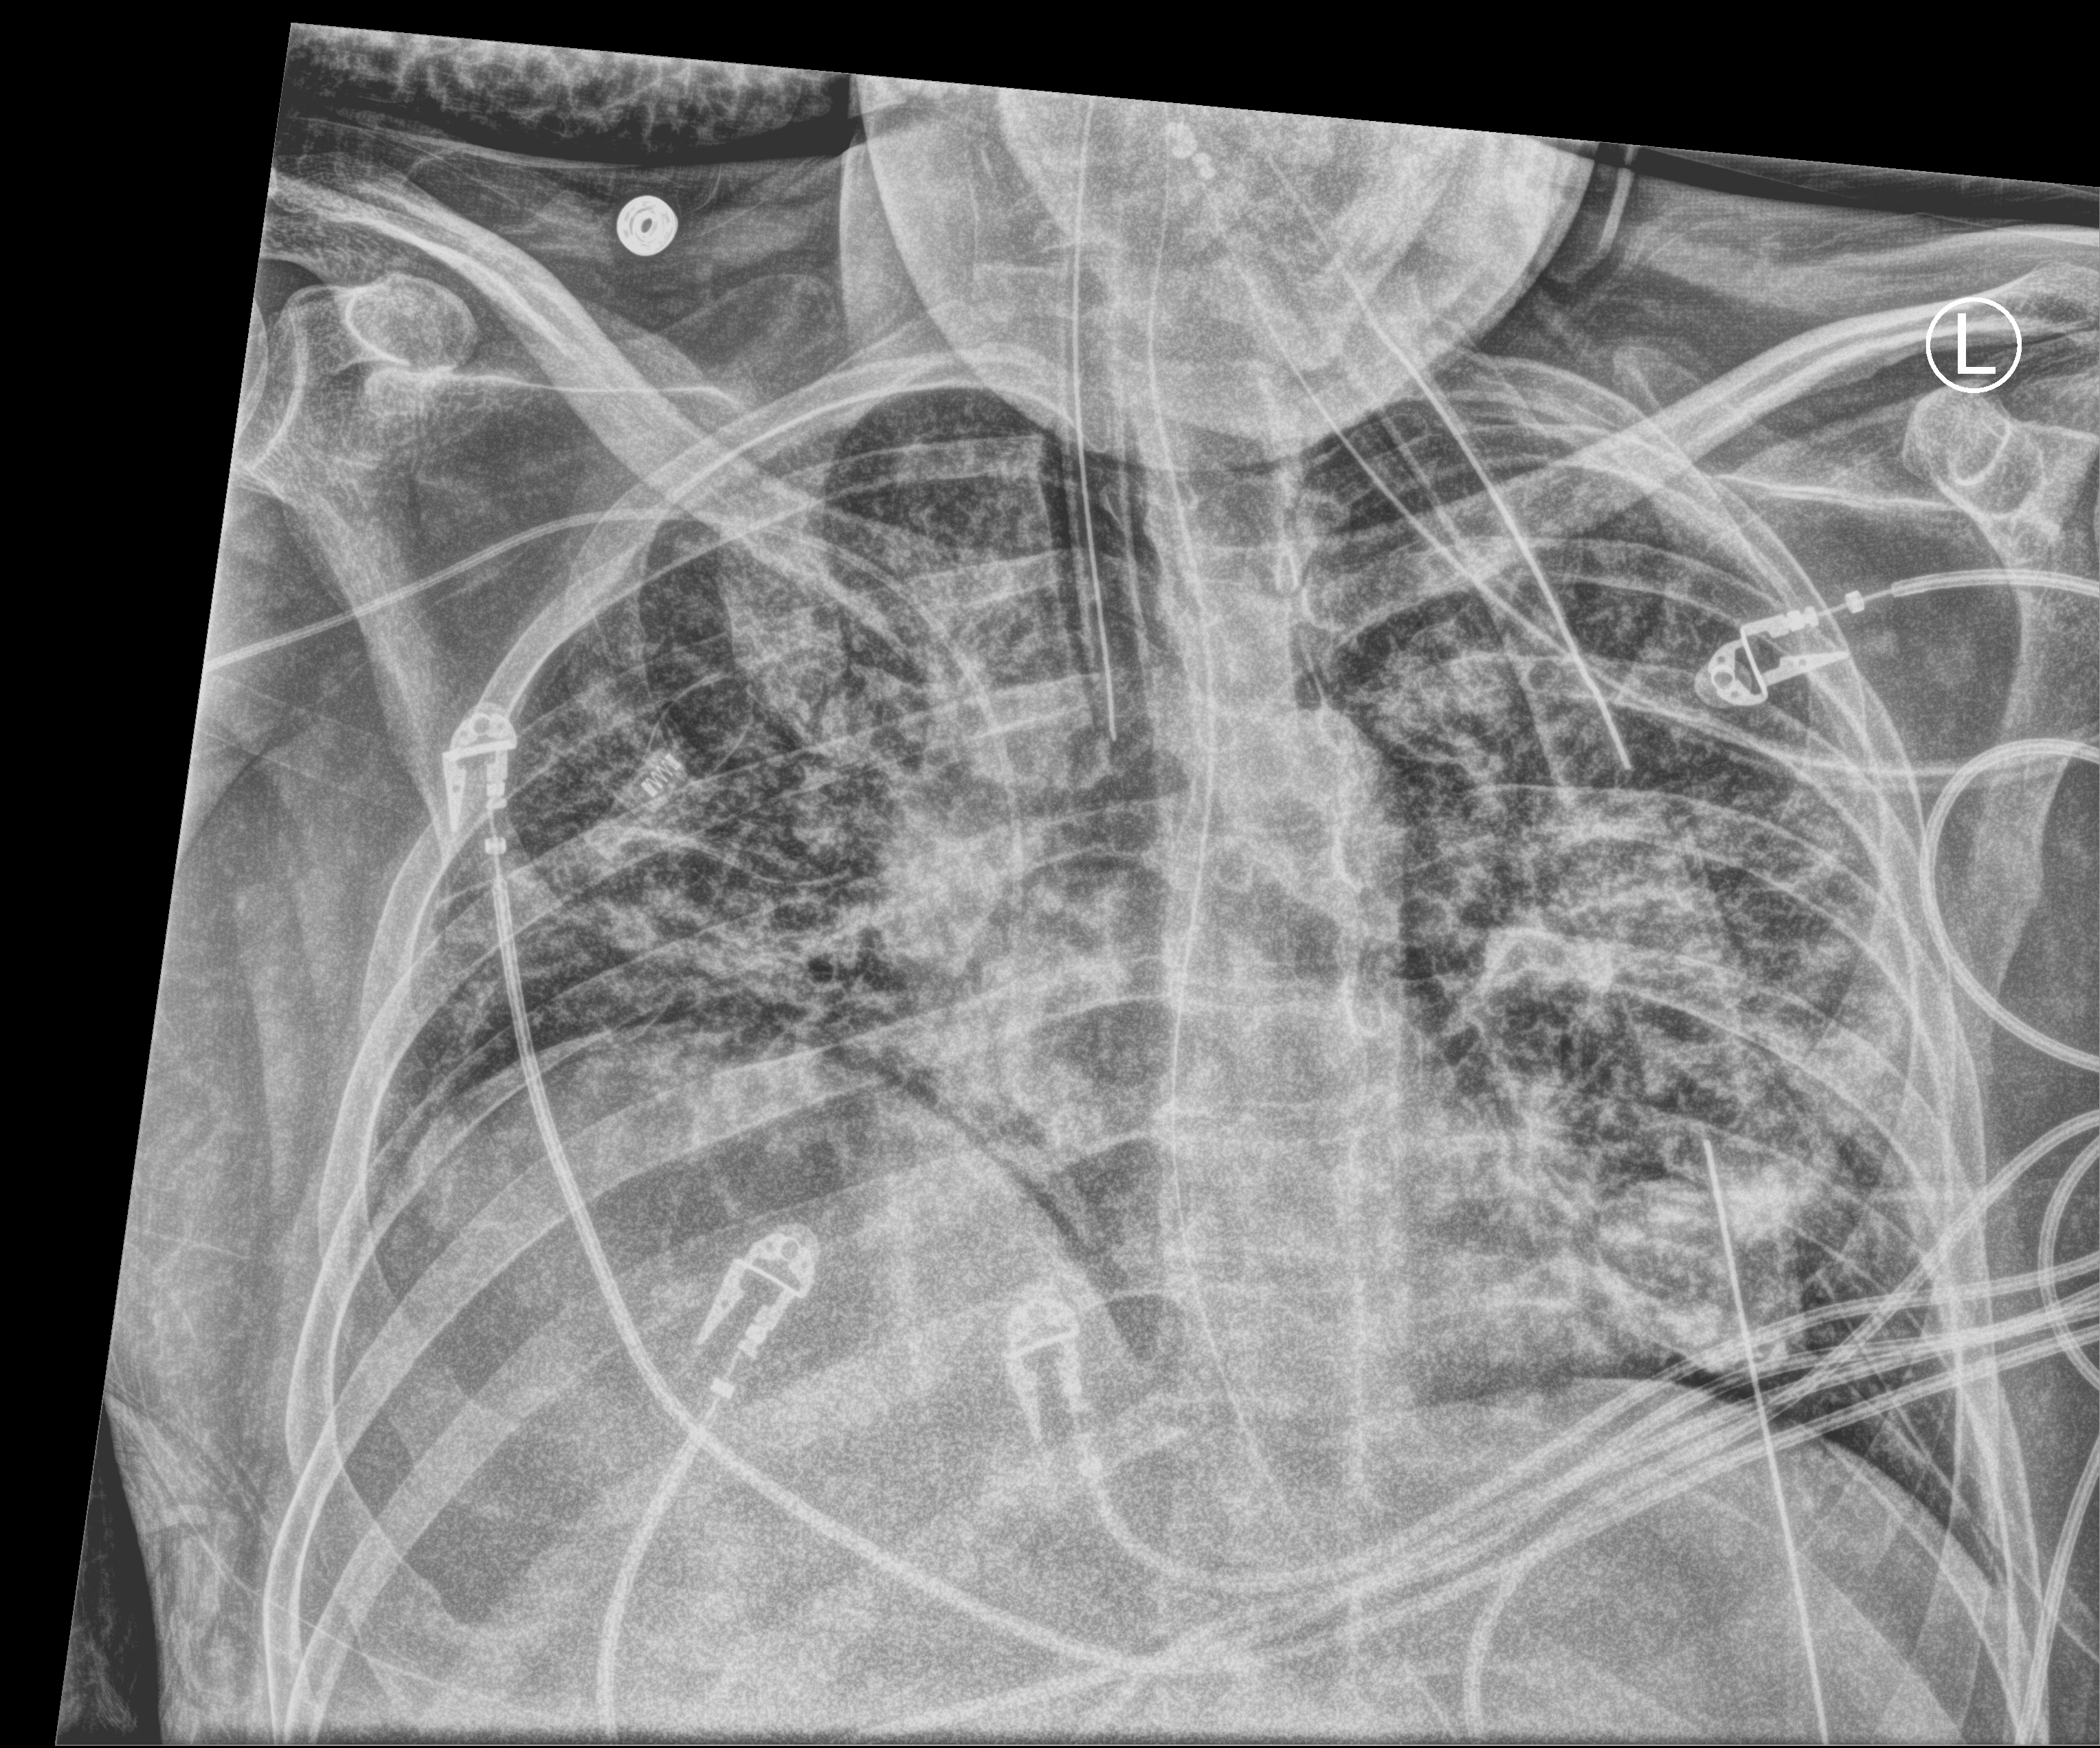
Chest X-ray (portable); anteroposterior (AP) projection. Patient hospitalised with COVID-19; male, aged 18–59 years.
Hospital-stay facts (about this admission, not read from this image; timing relative to this image not recorded): admitted to intensive care during this hospital stay: yes; chronic kidney disease (admission record): no.